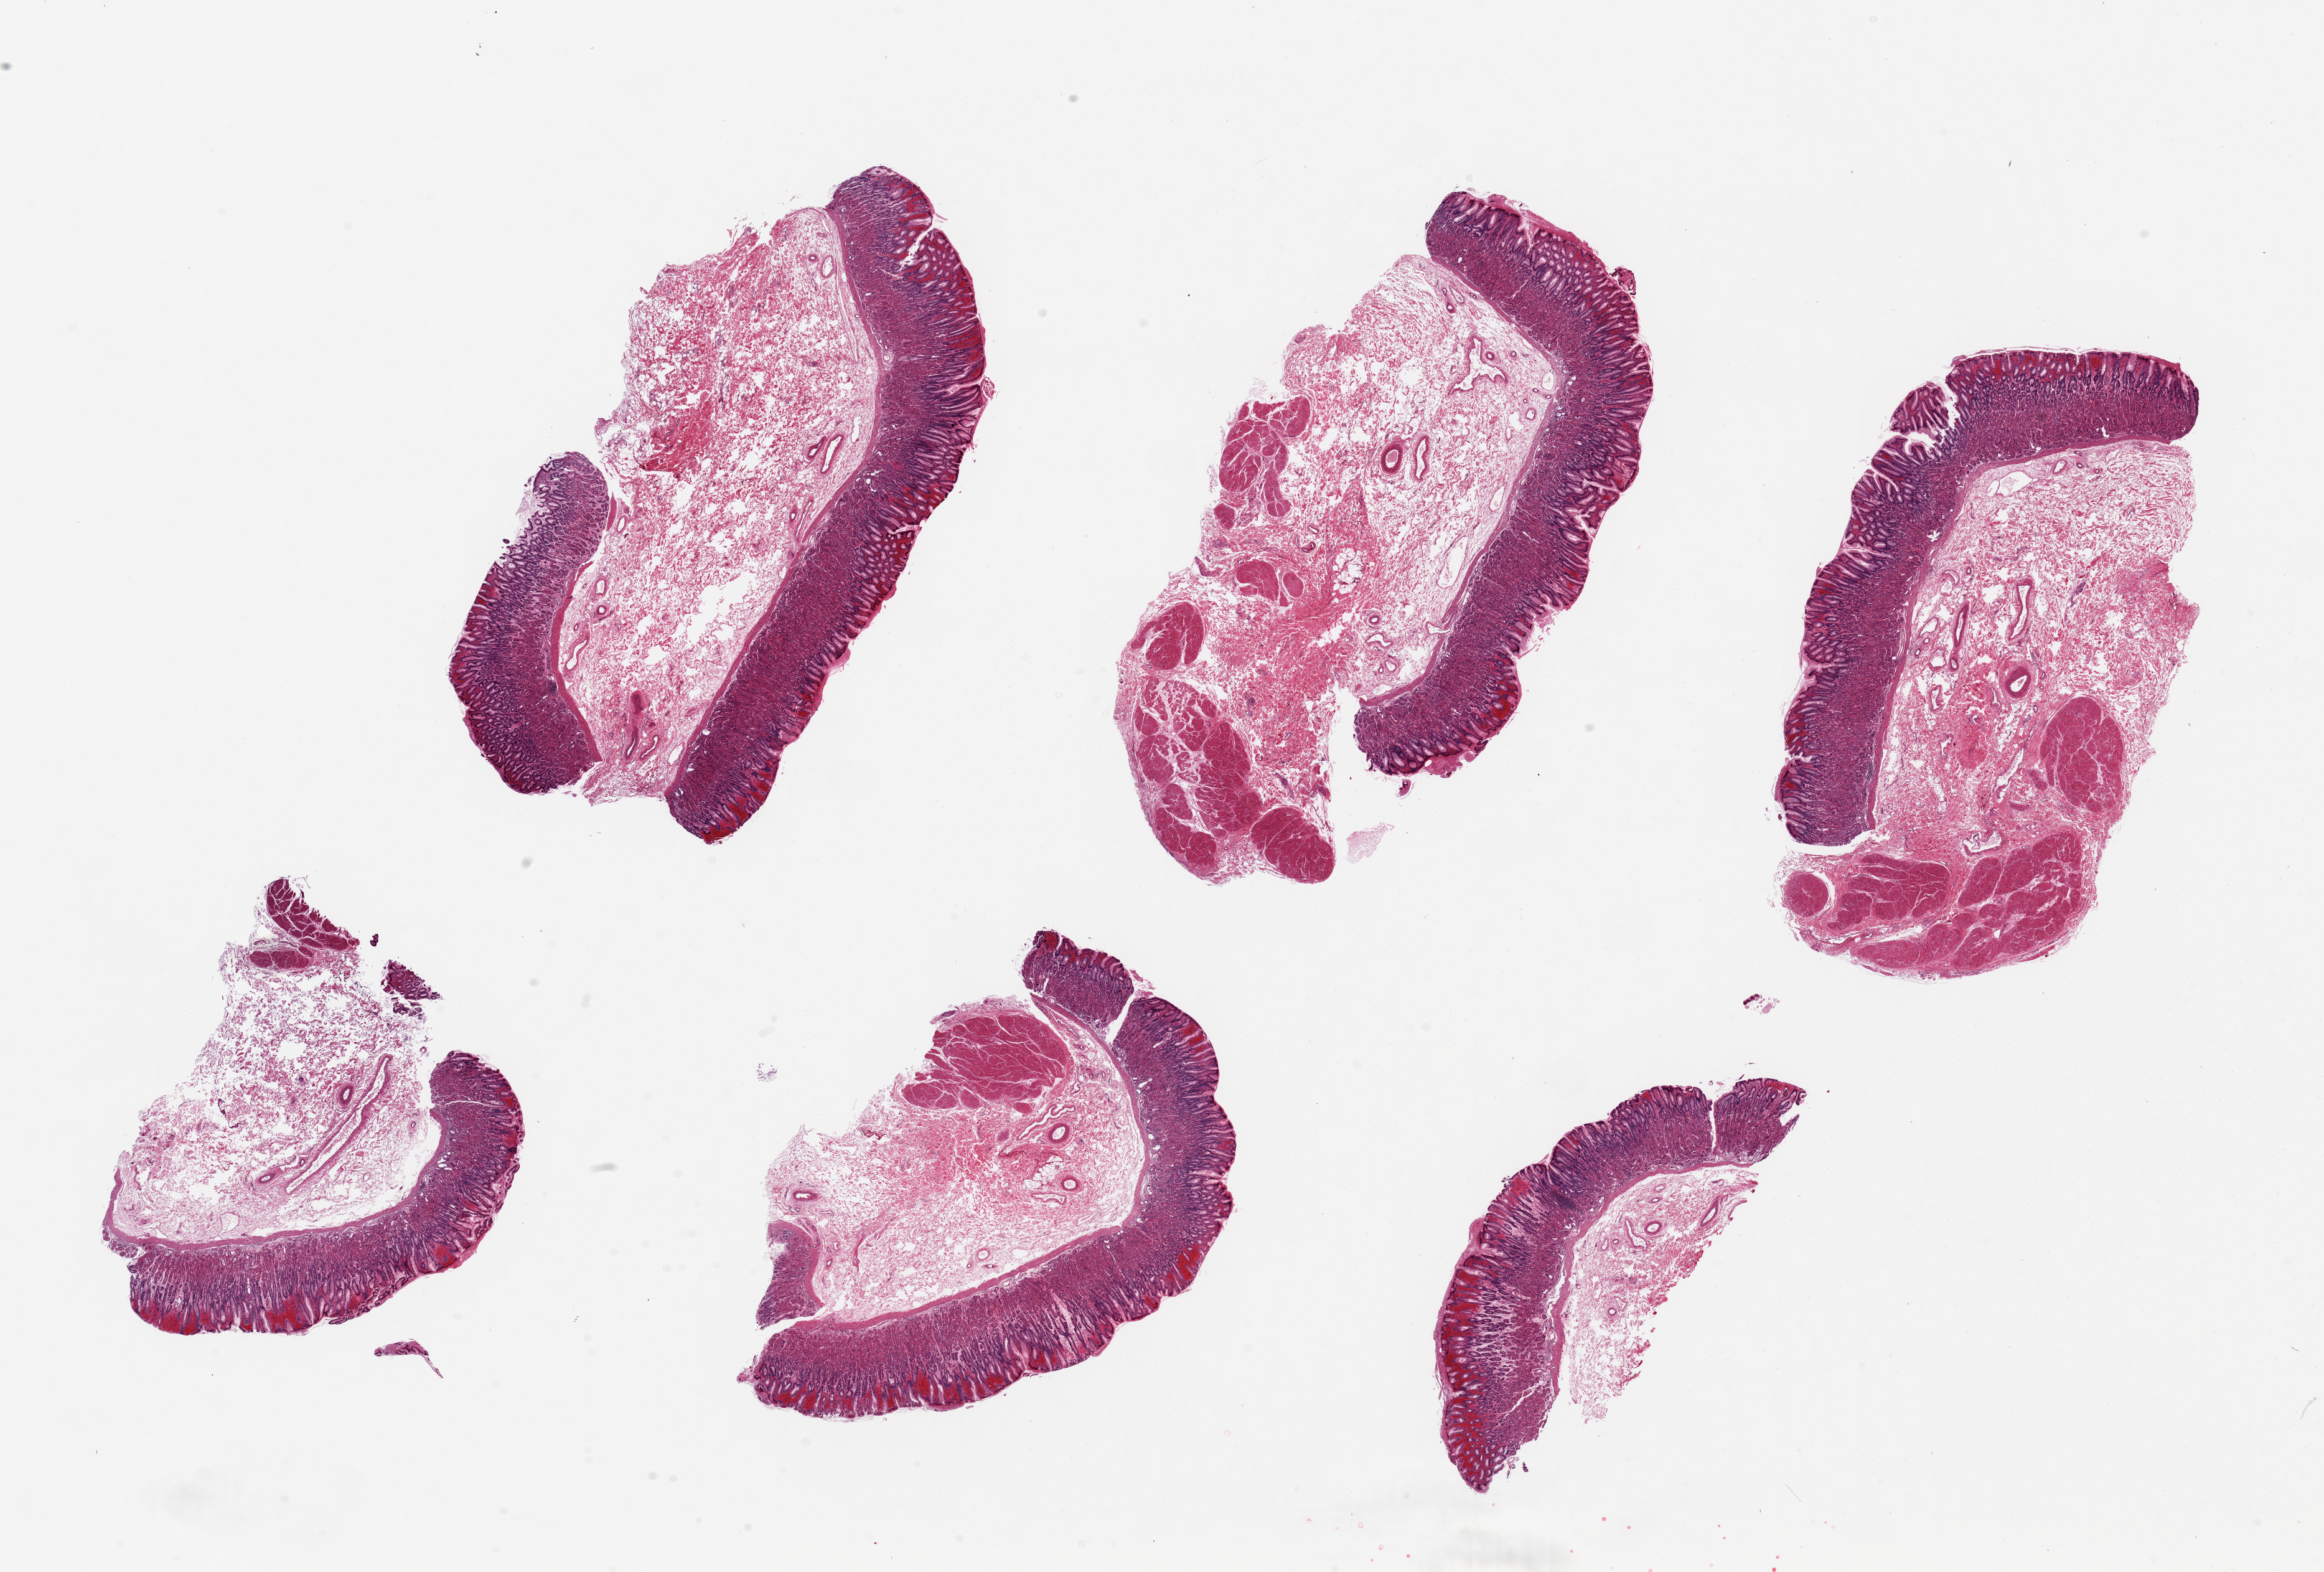
Whole-slide image, hematoxylin and eosin (H&E) stain, brightfield, a low-resolution overview of the entire scanned area, about 29.5 x 20.0 mm, PAXgene-fixed paraffin-embedded (PFPE) section, section of stomach (target tissue), tissue donor sample. Donor sex: male.
* reviewer comment on this tissue sample: 6 pieces ~9x5mm. Mucosa remarkably well-preserved ~25% of thickness